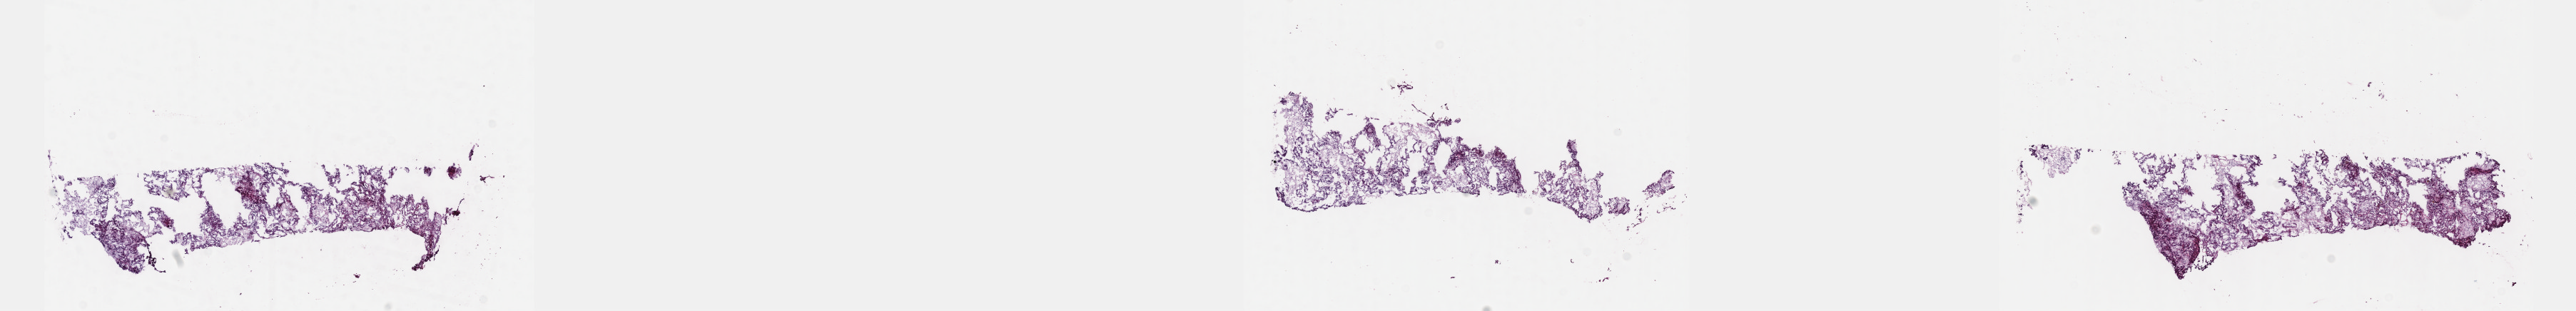
Digitized H&E tissue section (whole slide), low-resolution overview of the scanned area, about 29.2 x 3.5 mm (from a 40x scan), frozen section from the top of the tissue portion, sample: primary tumour, kidney. Patient: female, age at initial diagnosis 66 years. Slide review estimates, as recorded: tumour cells 100%, tumour nuclei 65%, normal cells 0%, stromal cells 0%, necrosis 0%. Infiltration values recorded for this section: lymphocyte infiltration 1%, monocyte infiltration 10%, neutrophil infiltration 0%.
- diagnosis: Papillary adenocarcinoma, NOS
- AJCC pathologic stage: I (7th edition)